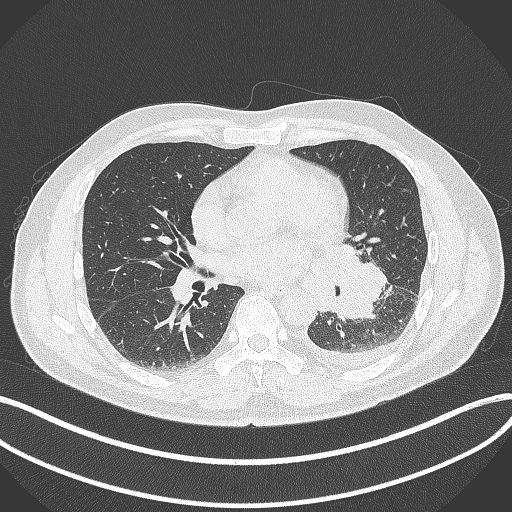
Chest CT, one axial slice. Slice 173 of 342 in the series (ordered by position). 120 kVp. Lung window (W 1500 / L -600 HU). 1 mm slice thickness. 512 × 512 image matrix, field of view 400 × 400 mm. Male patient, age 58 years. Case-level facts recorded for this patient, not image findings: clinical TNM (as recorded): T3 N1 M1b; histopathological grade: G3.
Outlined on this slice (bounding box drawn by a radiologist):
- lung tumour (recorded histology: small cell carcinoma): bounding box <317,239,390,321> (left, top, right, bottom; pixels)